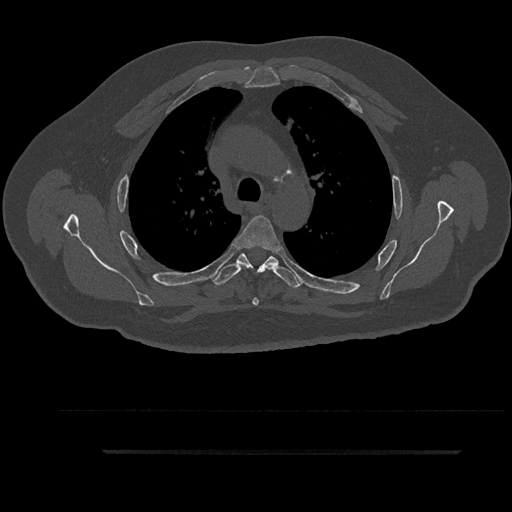
CT including the spine, one axial slice; position 652 of 797 along the scan axis; bone window (W 1800 / L 400 HU); 0.5 mm slice thickness; 512 × 512 image matrix. Male patient, age 63 years. Case-level facts recorded for this patient, not image findings: primary cancer: renal.
Outlined on this slice (semi-automatic segmentation, software-assisted and operator-edited):
- T3 vertebra: bounding box [x1, y1, x2, y2] px = [213, 256, 301, 286]
- T4 vertebra: [235, 215, 281, 306]
- T5 vertebra: [214, 253, 300, 289]